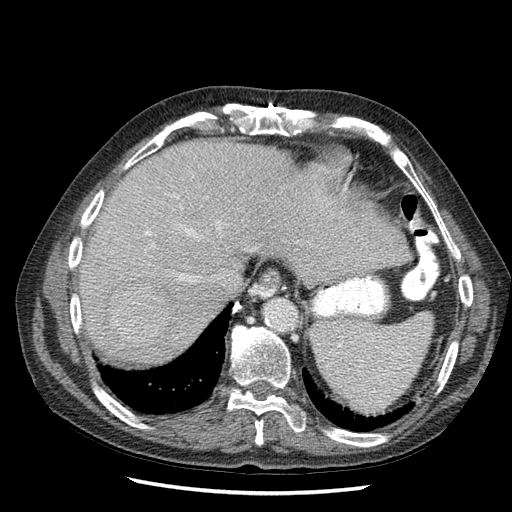
Contrast-enhanced abdominal CT (liver protocol), one axial slice; slice 48 of 67 in the series (ordered by position); 120 kVp; soft-tissue window (W 400 / L 40 HU); 2.5 mm slice thickness; 512 × 512 image matrix, field of view 360 × 360 mm. Case-level facts recorded for this patient, not image findings: diagnosis: hepatocellular carcinoma (patient treated with transarterial chemoembolisation; whether this scan precedes or follows treatment is not stated here); TNM stage (as recorded): Stage-I; Child-Pugh class: A; tumour differentiation: moderately differentiated; tumour nodularity: uninodular.
Structures marked on this image (semi-automatically segmented with operator editing):
- liver parenchyma outside the tumour (the mass and vessels are separate outlines, so this box may not span the whole liver): bounding box <80,138,414,363> (left, top, right, bottom; pixels)
- mass: <111,287,172,346>
- liver vessels: <145,196,232,293>